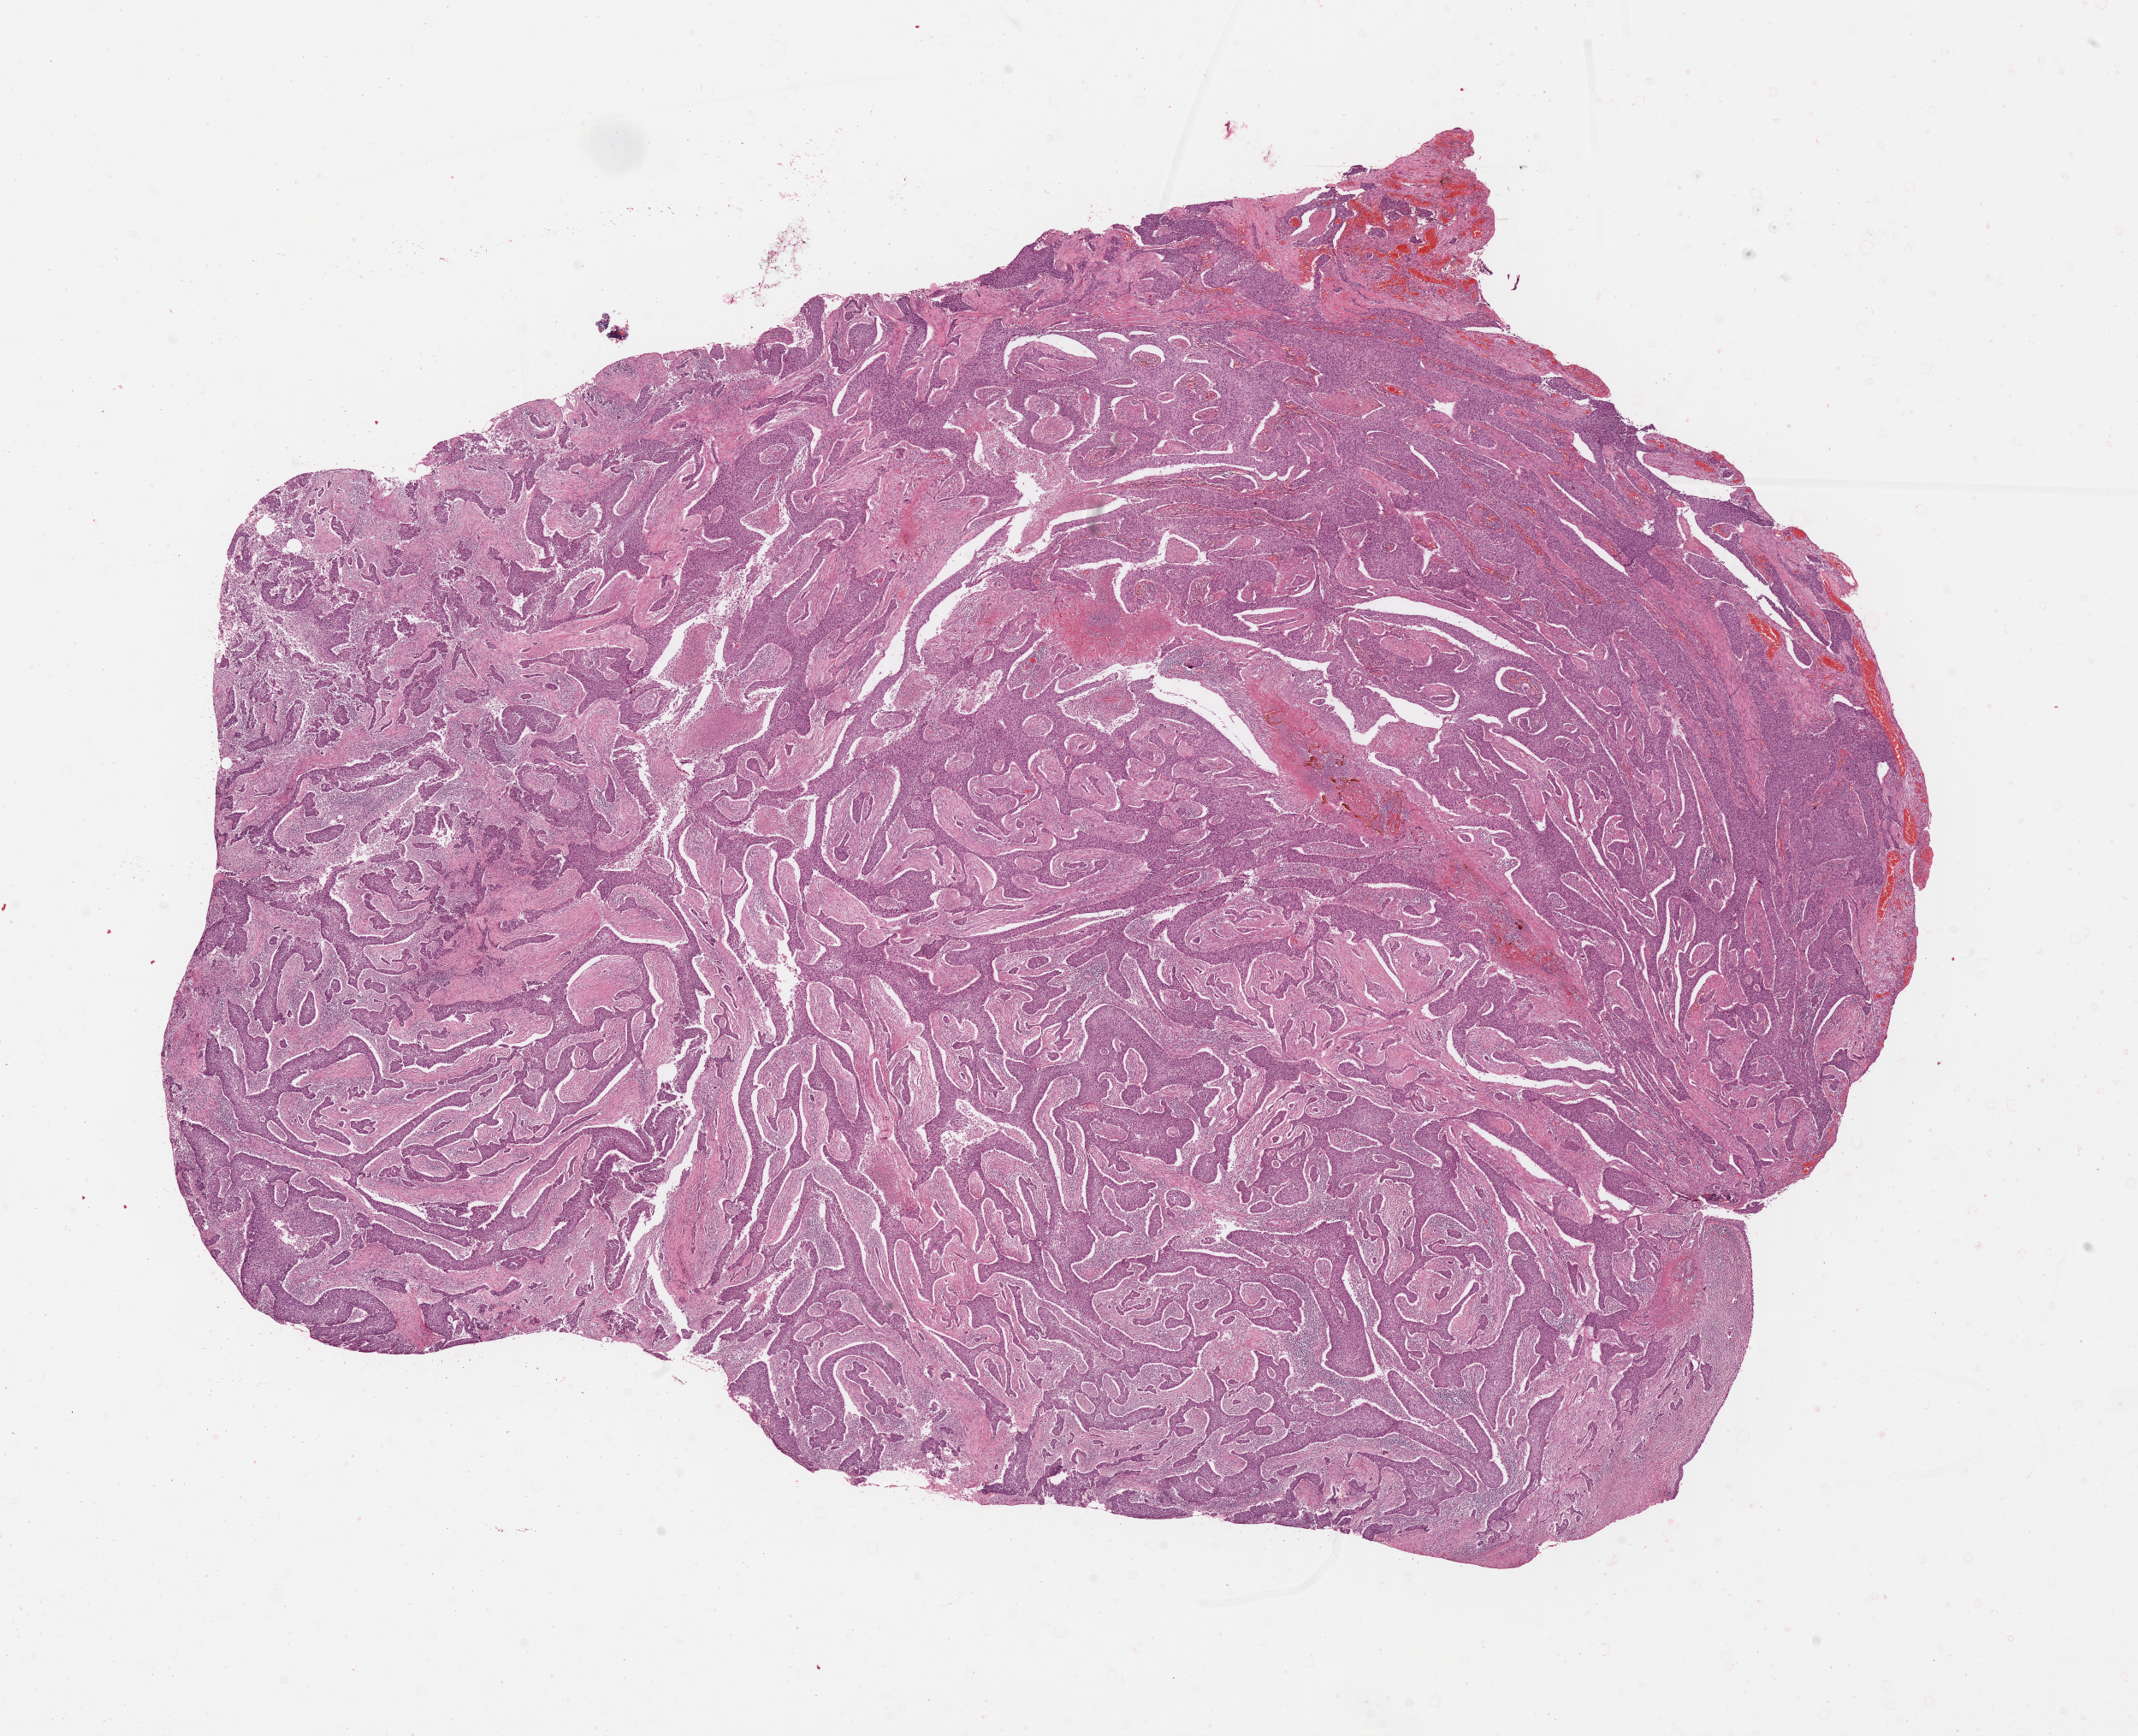
Hematoxylin and eosin (H&E) stained whole-slide image — whole scanned area (about 19.6 x 15.9 mm, slide scanned at 40x) shown as a low-resolution overview; formalin-fixed paraffin-embedded (FFPE) diagnostic section; sample: primary tumour, bladder. Male, age 59 years at initial diagnosis. Histologic grade: high grade.
Lymph nodes positive (case pathology): 0 of 8 examined. Pathologic diagnosis: Transitional cell carcinoma. AJCC pathologic stage: II (7th edition).